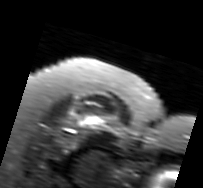
MRI of an extremity soft-tissue mass, one axial slice; slice 66 of 91 in the series (ordered by position); T2-weighted fat-saturated; MR volume resampled by the dataset authors to the PET/CT grid (not the native acquisition matrix); 3.27 mm slice thickness; 203 × 188 image matrix, field of view 198 × 184 mm. Female patient. From the clinical record (not read from this slice): histological type: malignant solitary fibrous tumor; grade: intermediate; site of the primary tumour: right thigh.
Outlined on this slice (expert contour drawn on MRI and transferred to this co-registered scan by the dataset authors):
- gross tumour volume including surrounding oedema: bounding box [x1, y1, x2, y2] px = [60, 110, 123, 148]